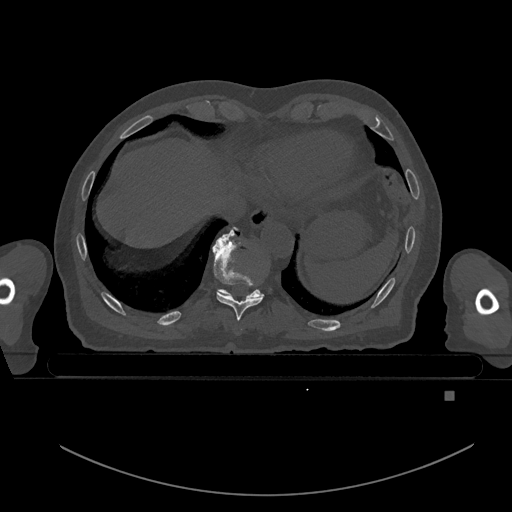
CT including the spine, one axial slice; slice 130 of 969 in the series (ordered by position); bone window (W 1800 / L 400 HU); 0.5 mm slice thickness; 512 × 512 image matrix. Patient: male, 82 years. Case-level facts recorded for this patient, not image findings: primary cancer: prostate.
Annotated regions visible in this slice (semi-automatic segmentation, software-assisted and operator-edited):
- T10 vertebra: bounding box (x1, y1, x2, y2) in pixels: (220, 227, 261, 297)
- T9 vertebra: (213, 230, 264, 320)